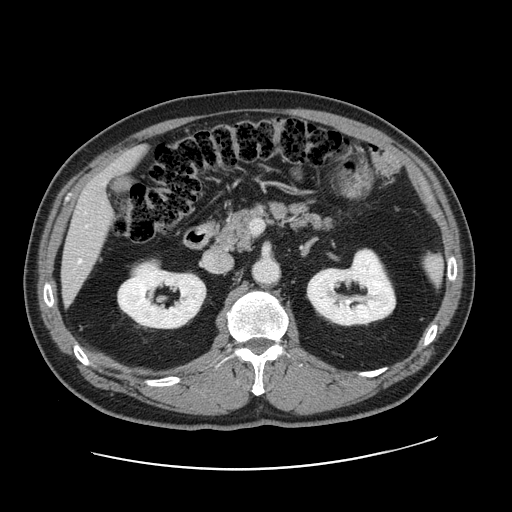
Contrast-enhanced abdominal CT, one axial slice; intravenous contrast given; soft-tissue window (W 400 / L 40 HU); 512 × 512 image matrix. Male patient, age 63 years. Case-level facts recorded for this patient, not image findings: diagnosis: colorectal cancer liver metastases, imaged before liver resection; multiple liver metastases: yes; largest metastasis: 8 cm.
Structures marked on this image (manually delineated by an expert):
- hepatic veins: bounding box (x1, y1, x2, y2) in pixels: (79, 225, 88, 262)
- liver: (62, 150, 142, 299)
- planned liver remnant (the part of the liver to remain after resection): (111, 150, 142, 171)